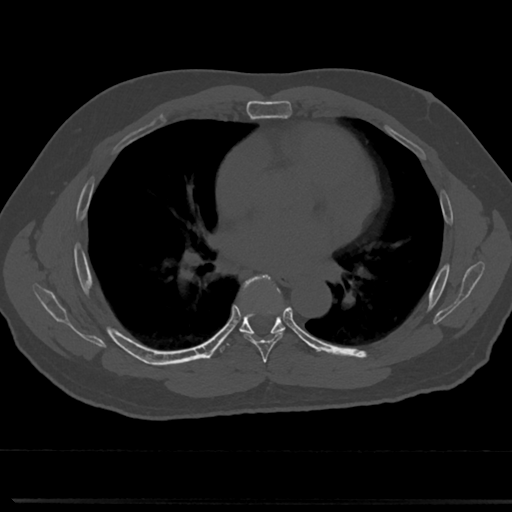
CT including the spine, one axial slice; slice 431 of 817 in the series (ordered by position); reconstruction kernel Br40s/3; 120 kVp; bone window (W 1800 / L 400 HU); 0.5 mm slice thickness; 512 × 512 image matrix, field of view 355 × 355 mm. Patient: male, 61 years. From the clinical record (not read from this slice): primary cancer: prostate.
Annotated regions visible in this slice (semi-automatic segmentation, software-assisted and operator-edited):
- T5 vertebra: bounding box (x1, y1, x2, y2) in pixels: (265, 370, 271, 376)
- T6 vertebra: (237, 276, 290, 356)
- T7 vertebra: (241, 326, 283, 334)